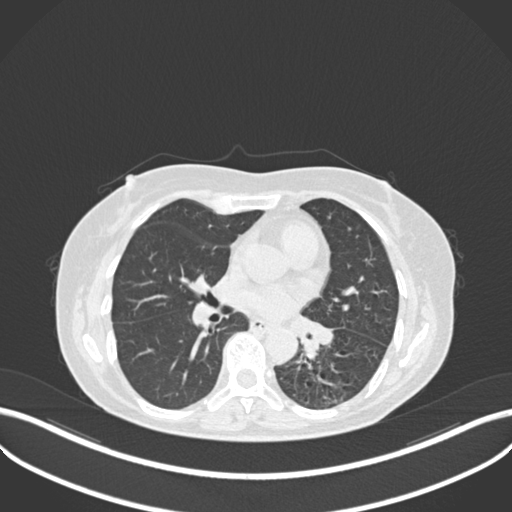
Chest CT, one axial slice; position 130 of 270 along the scan axis; lung window (W 1500 / L -600 HU); 1 mm slice thickness; 512 × 512 image matrix, field of view 400 × 400 mm. Female patient, age 63 years. From the clinical record (not read from this slice): clinical TNM (as recorded): T1b N0 M0; histopathological grade: G2-3.
Outlined on this slice (rectangle marked by the reading radiologist):
- lung tumour (recorded histology: adenocarcinoma): bounding box [x1, y1, x2, y2] px = [291, 311, 336, 363]